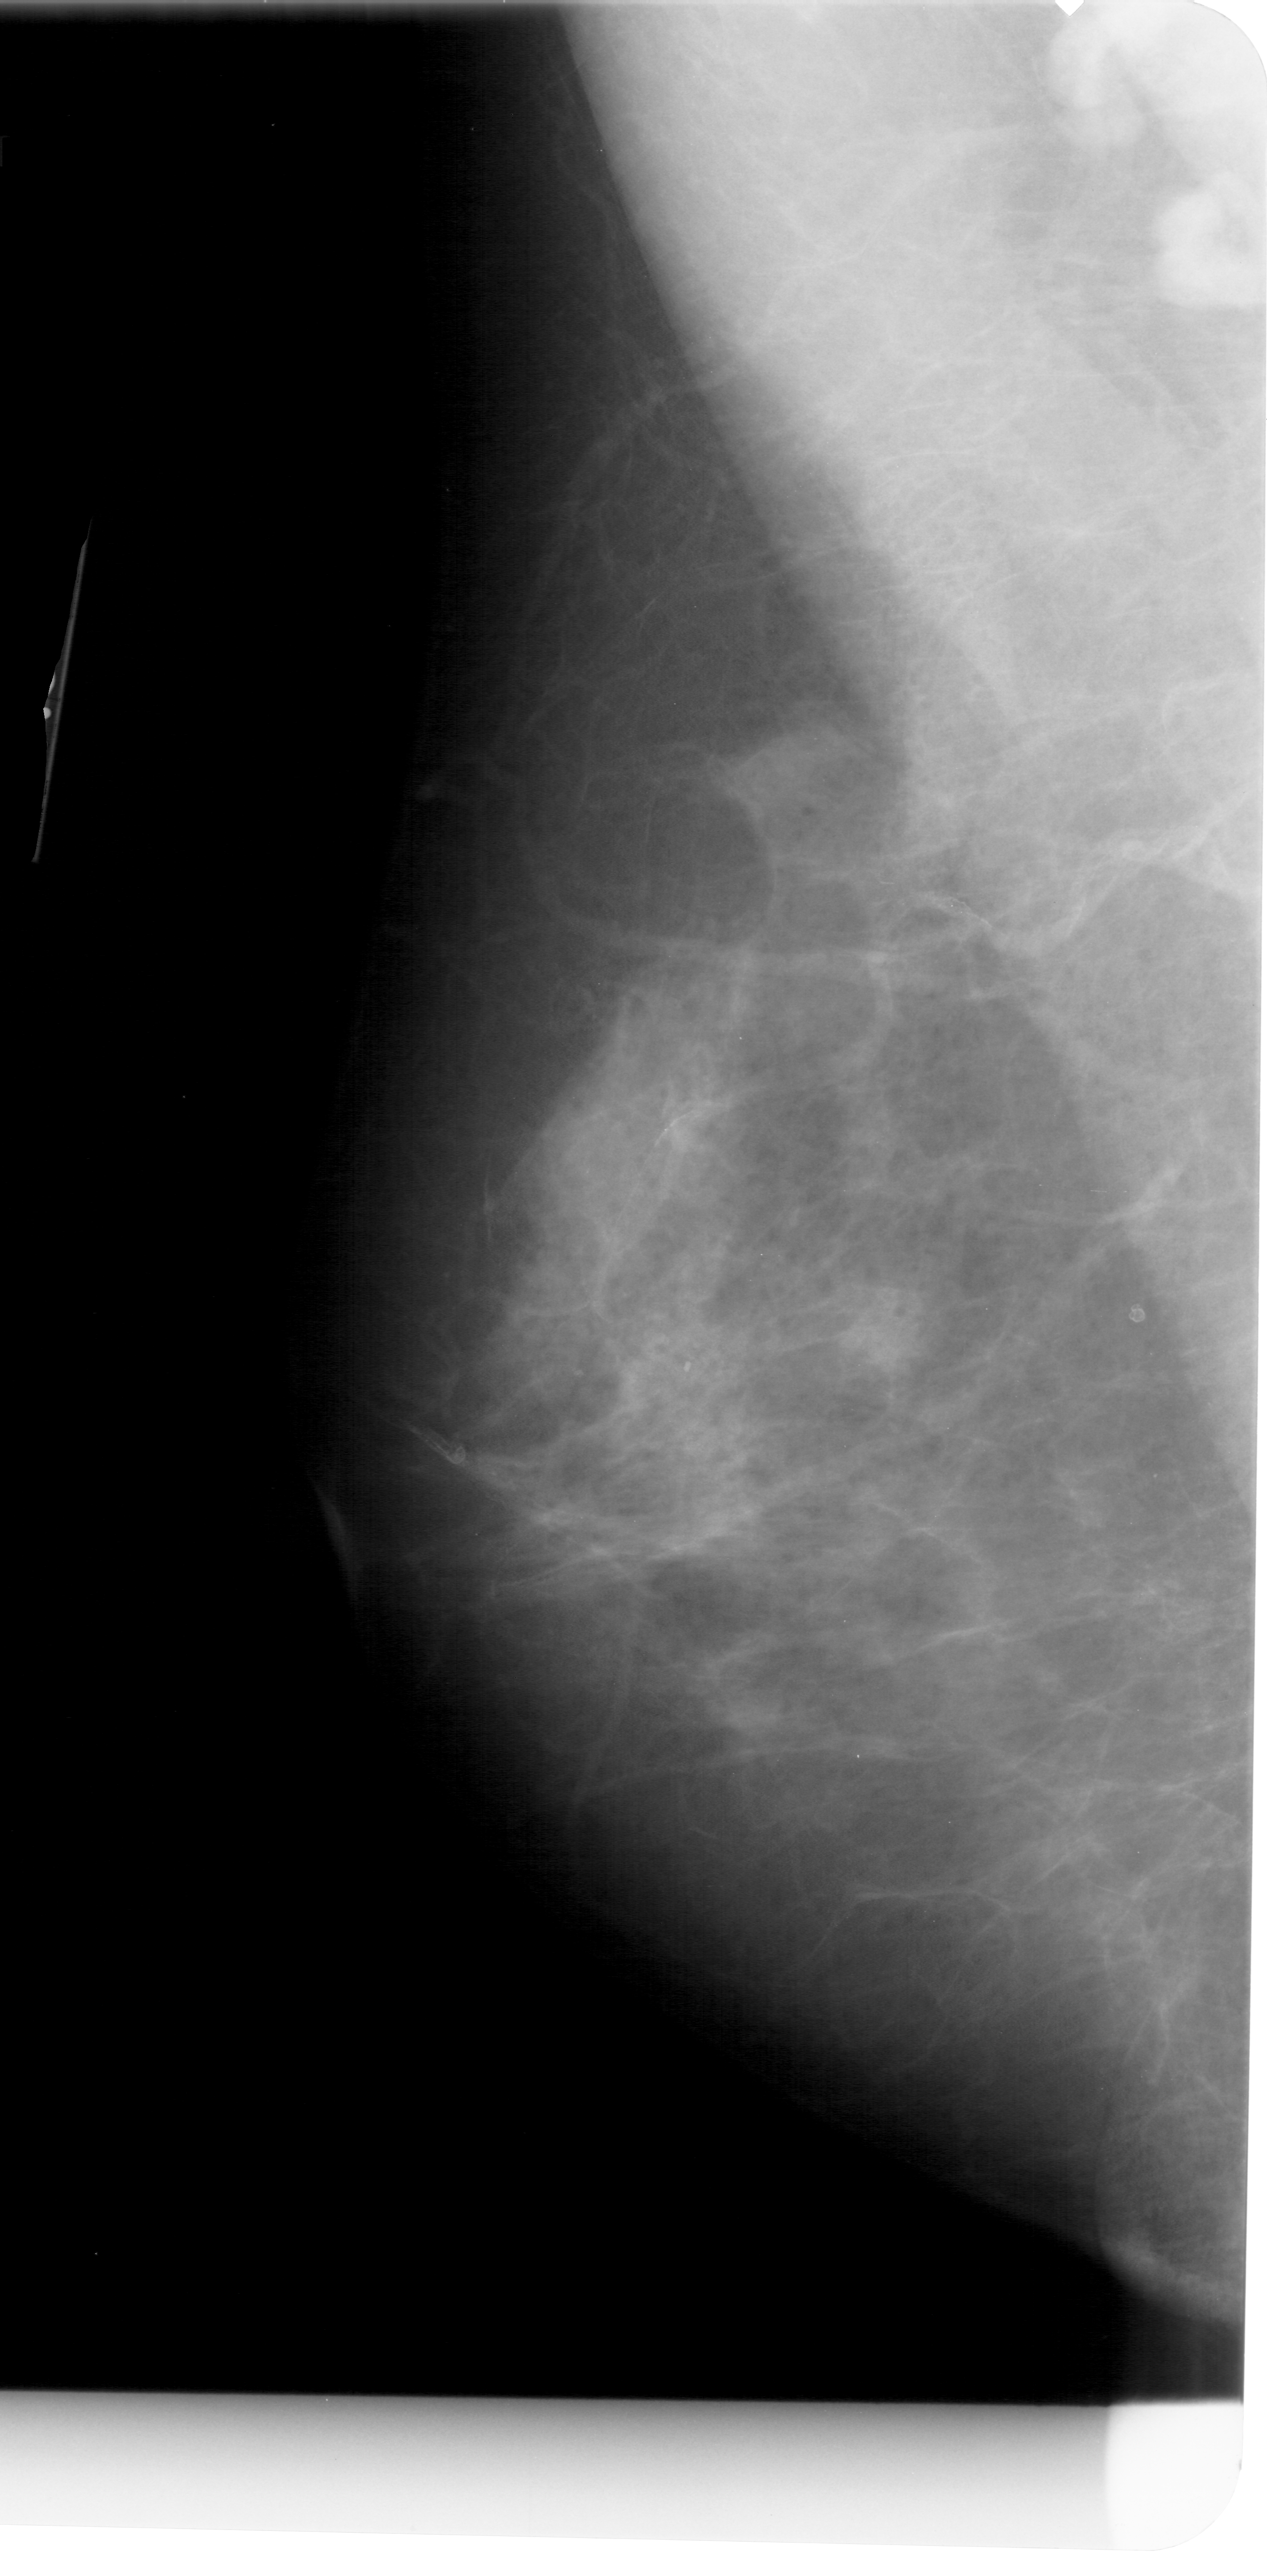
Mammogram (digitized film), left breast, mediolateral oblique (MLO) view, BI-RADS breast density category 4 (scale 1–4).
Radiologist-marked abnormalities on this image: mass, shape irregular, margins ill defined; BI-RADS assessment category 4; pathology result (as recorded, not read from the image): benign.